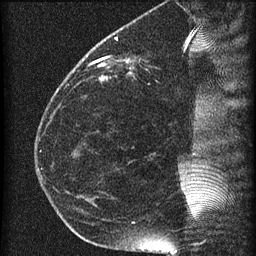
Breast MRI (dynamic contrast-enhanced), one sagittal slice; slice 21 of 60 in the series (ordered by position); dynamic contrast-enhanced series, image 2 of 4 at this slice position (ordered by acquisition); 1.5 T; TE 4.2 ms, TR 22.7 ms; 1.5 mm slice thickness; 256 × 256 image matrix. Female patient, age 35 years. From the clinical record (not read from this slice): setting: breast cancer imaged before/during neoadjuvant chemotherapy; receptor status: HR-positive, HER2-negative.
Structures marked on this image (semi-automatic segmentation, software-assisted and operator-edited):
- analysis volume of interest (the breast-tissue region the enhancement analysis was run in; not a lesion): bounding box [x1, y1, x2, y2] px = [69, 27, 199, 112]
- tumour enhancement mask (voxels above the 90 % enhancement threshold inside the analysis volume of interest): [89, 57, 109, 66]